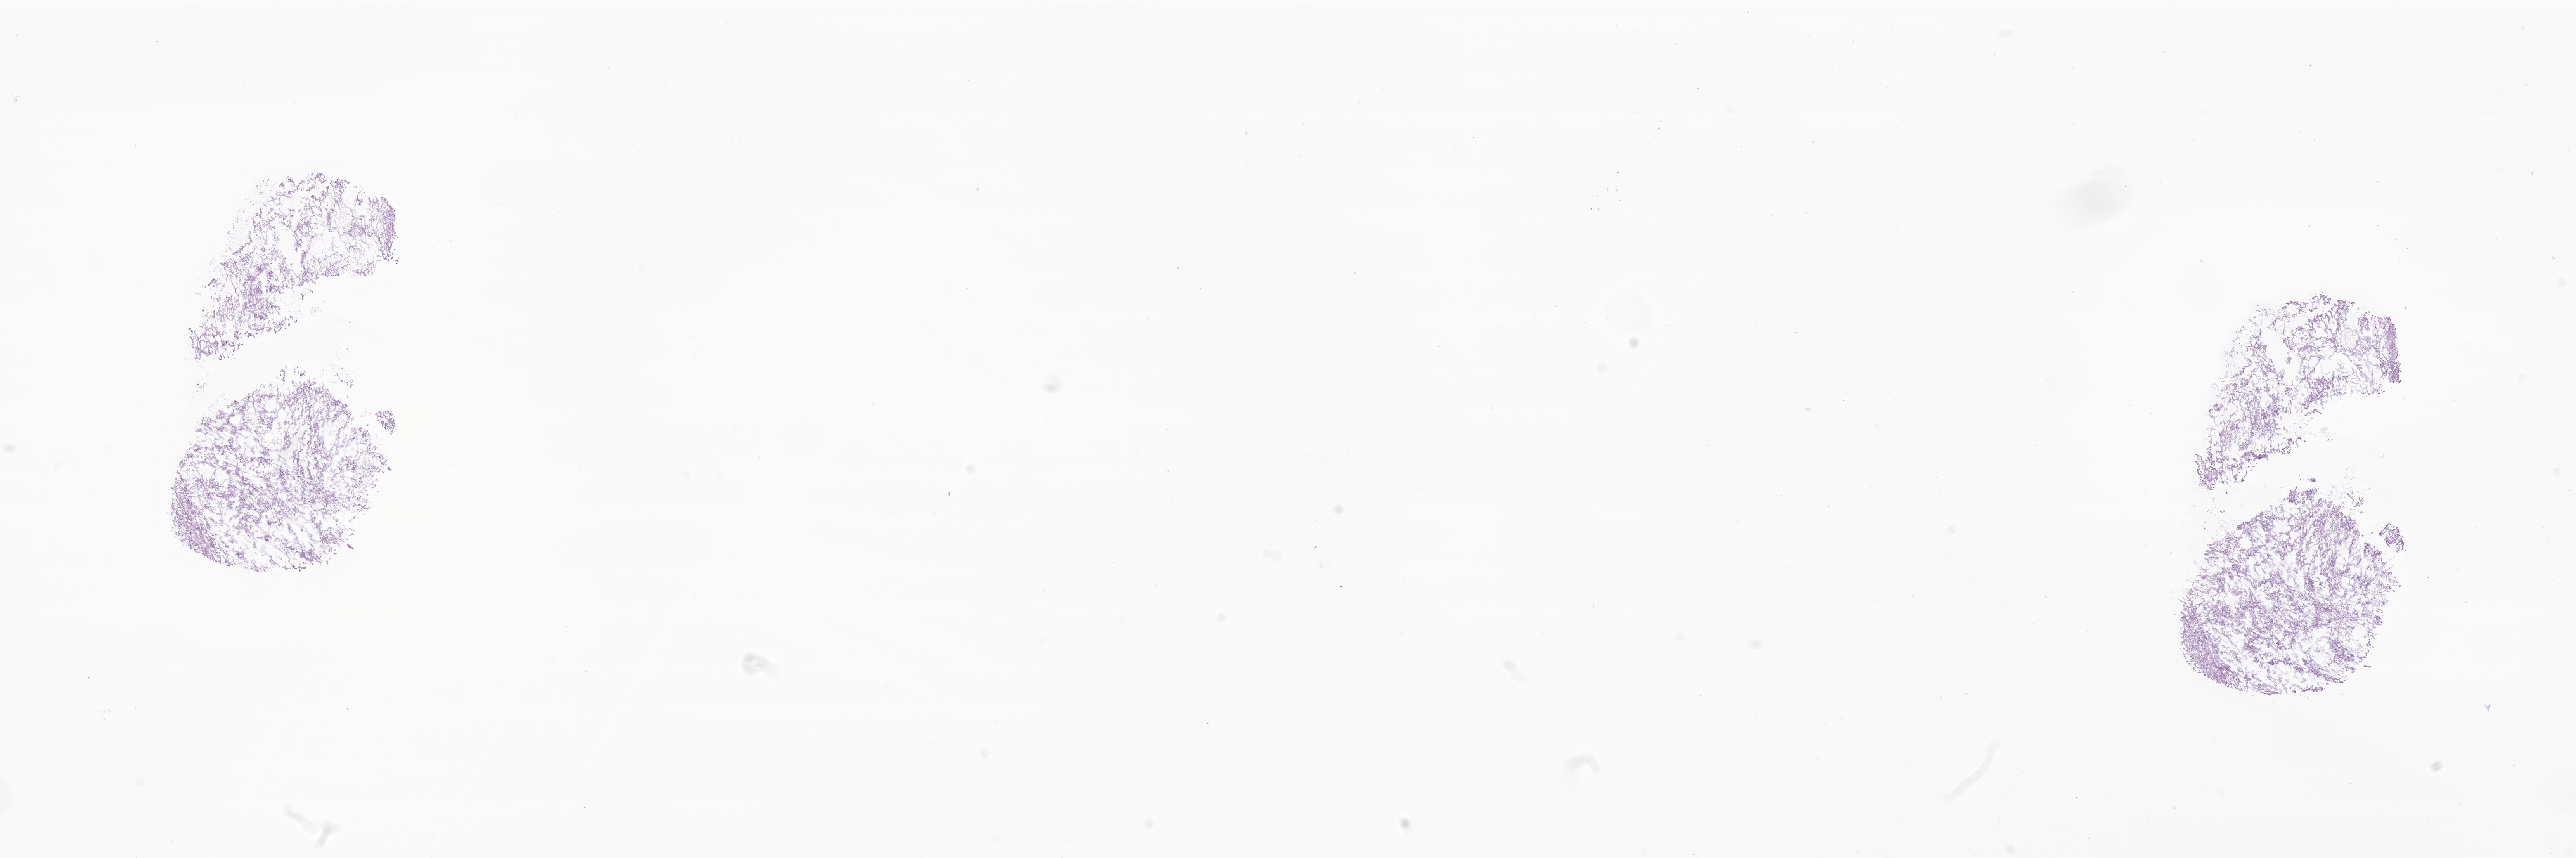
Digitized haematoxylin and eosin-stained section of tumor tissue from the brain, whole scanned area (about 28.0 x 9.3 mm) shown as a low-resolution overview. Frozen section (OCT-embedded). Patient: female, age 204 months (17 years).
Diagnosis: Neoplasm, uncertain whether benign or malignant.